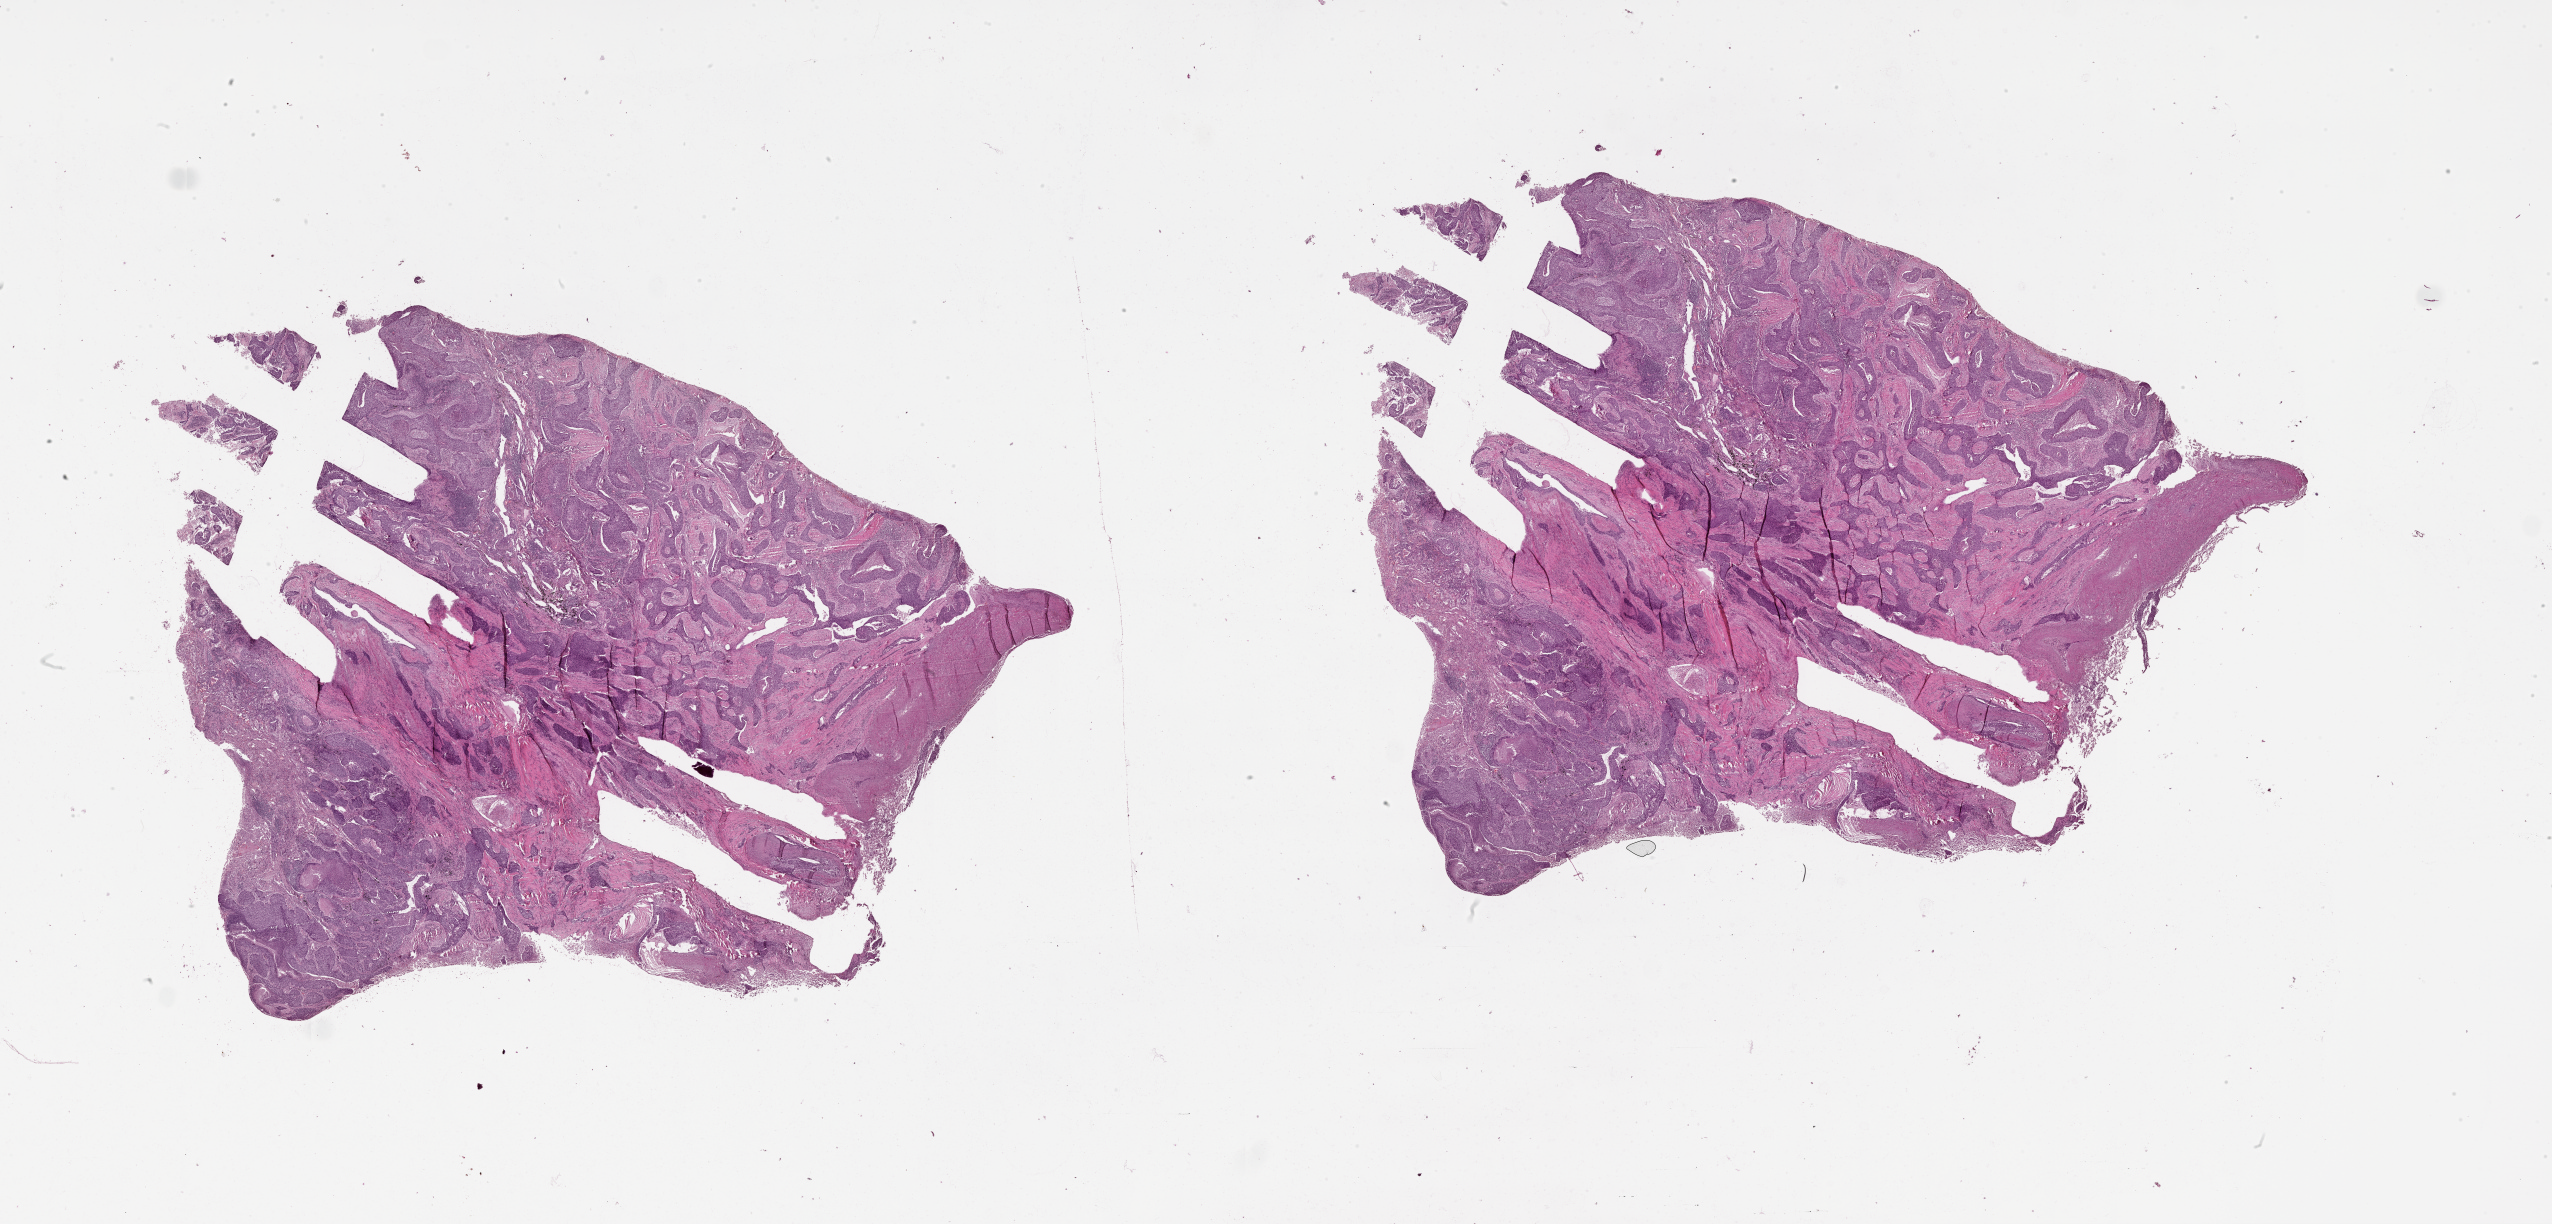
Digitized H&E tissue section (whole slide), whole scanned area (about 41.1 x 19.7 mm, slide scanned at 20x) shown as a low-resolution overview; tumour tissue sample, lung. Patient: male, age 63 years.
* patient diagnosis (cohort enrolment): squamous cell carcinoma (lung)